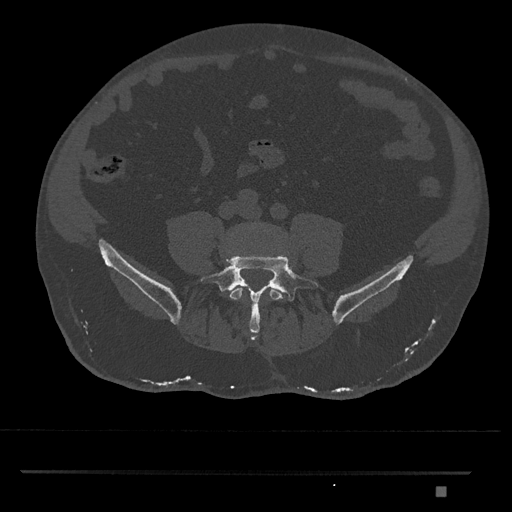
CT including the spine, one axial slice. Position 573 of 1134 along the scan axis. 120 kVp. Bone window (W 1800 / L 400 HU). 0.5 mm slice thickness. 512 × 512 image matrix, field of view 429 × 429 mm. Male patient, age 65 years. From the clinical record (not read from this slice): primary cancer: prostate.
Outlined on this slice (semi-automatically segmented with operator editing):
- L4 vertebra: bounding box (x1, y1, x2, y2) in pixels: (229, 287, 285, 300)
- L5 vertebra: (200, 254, 322, 337)